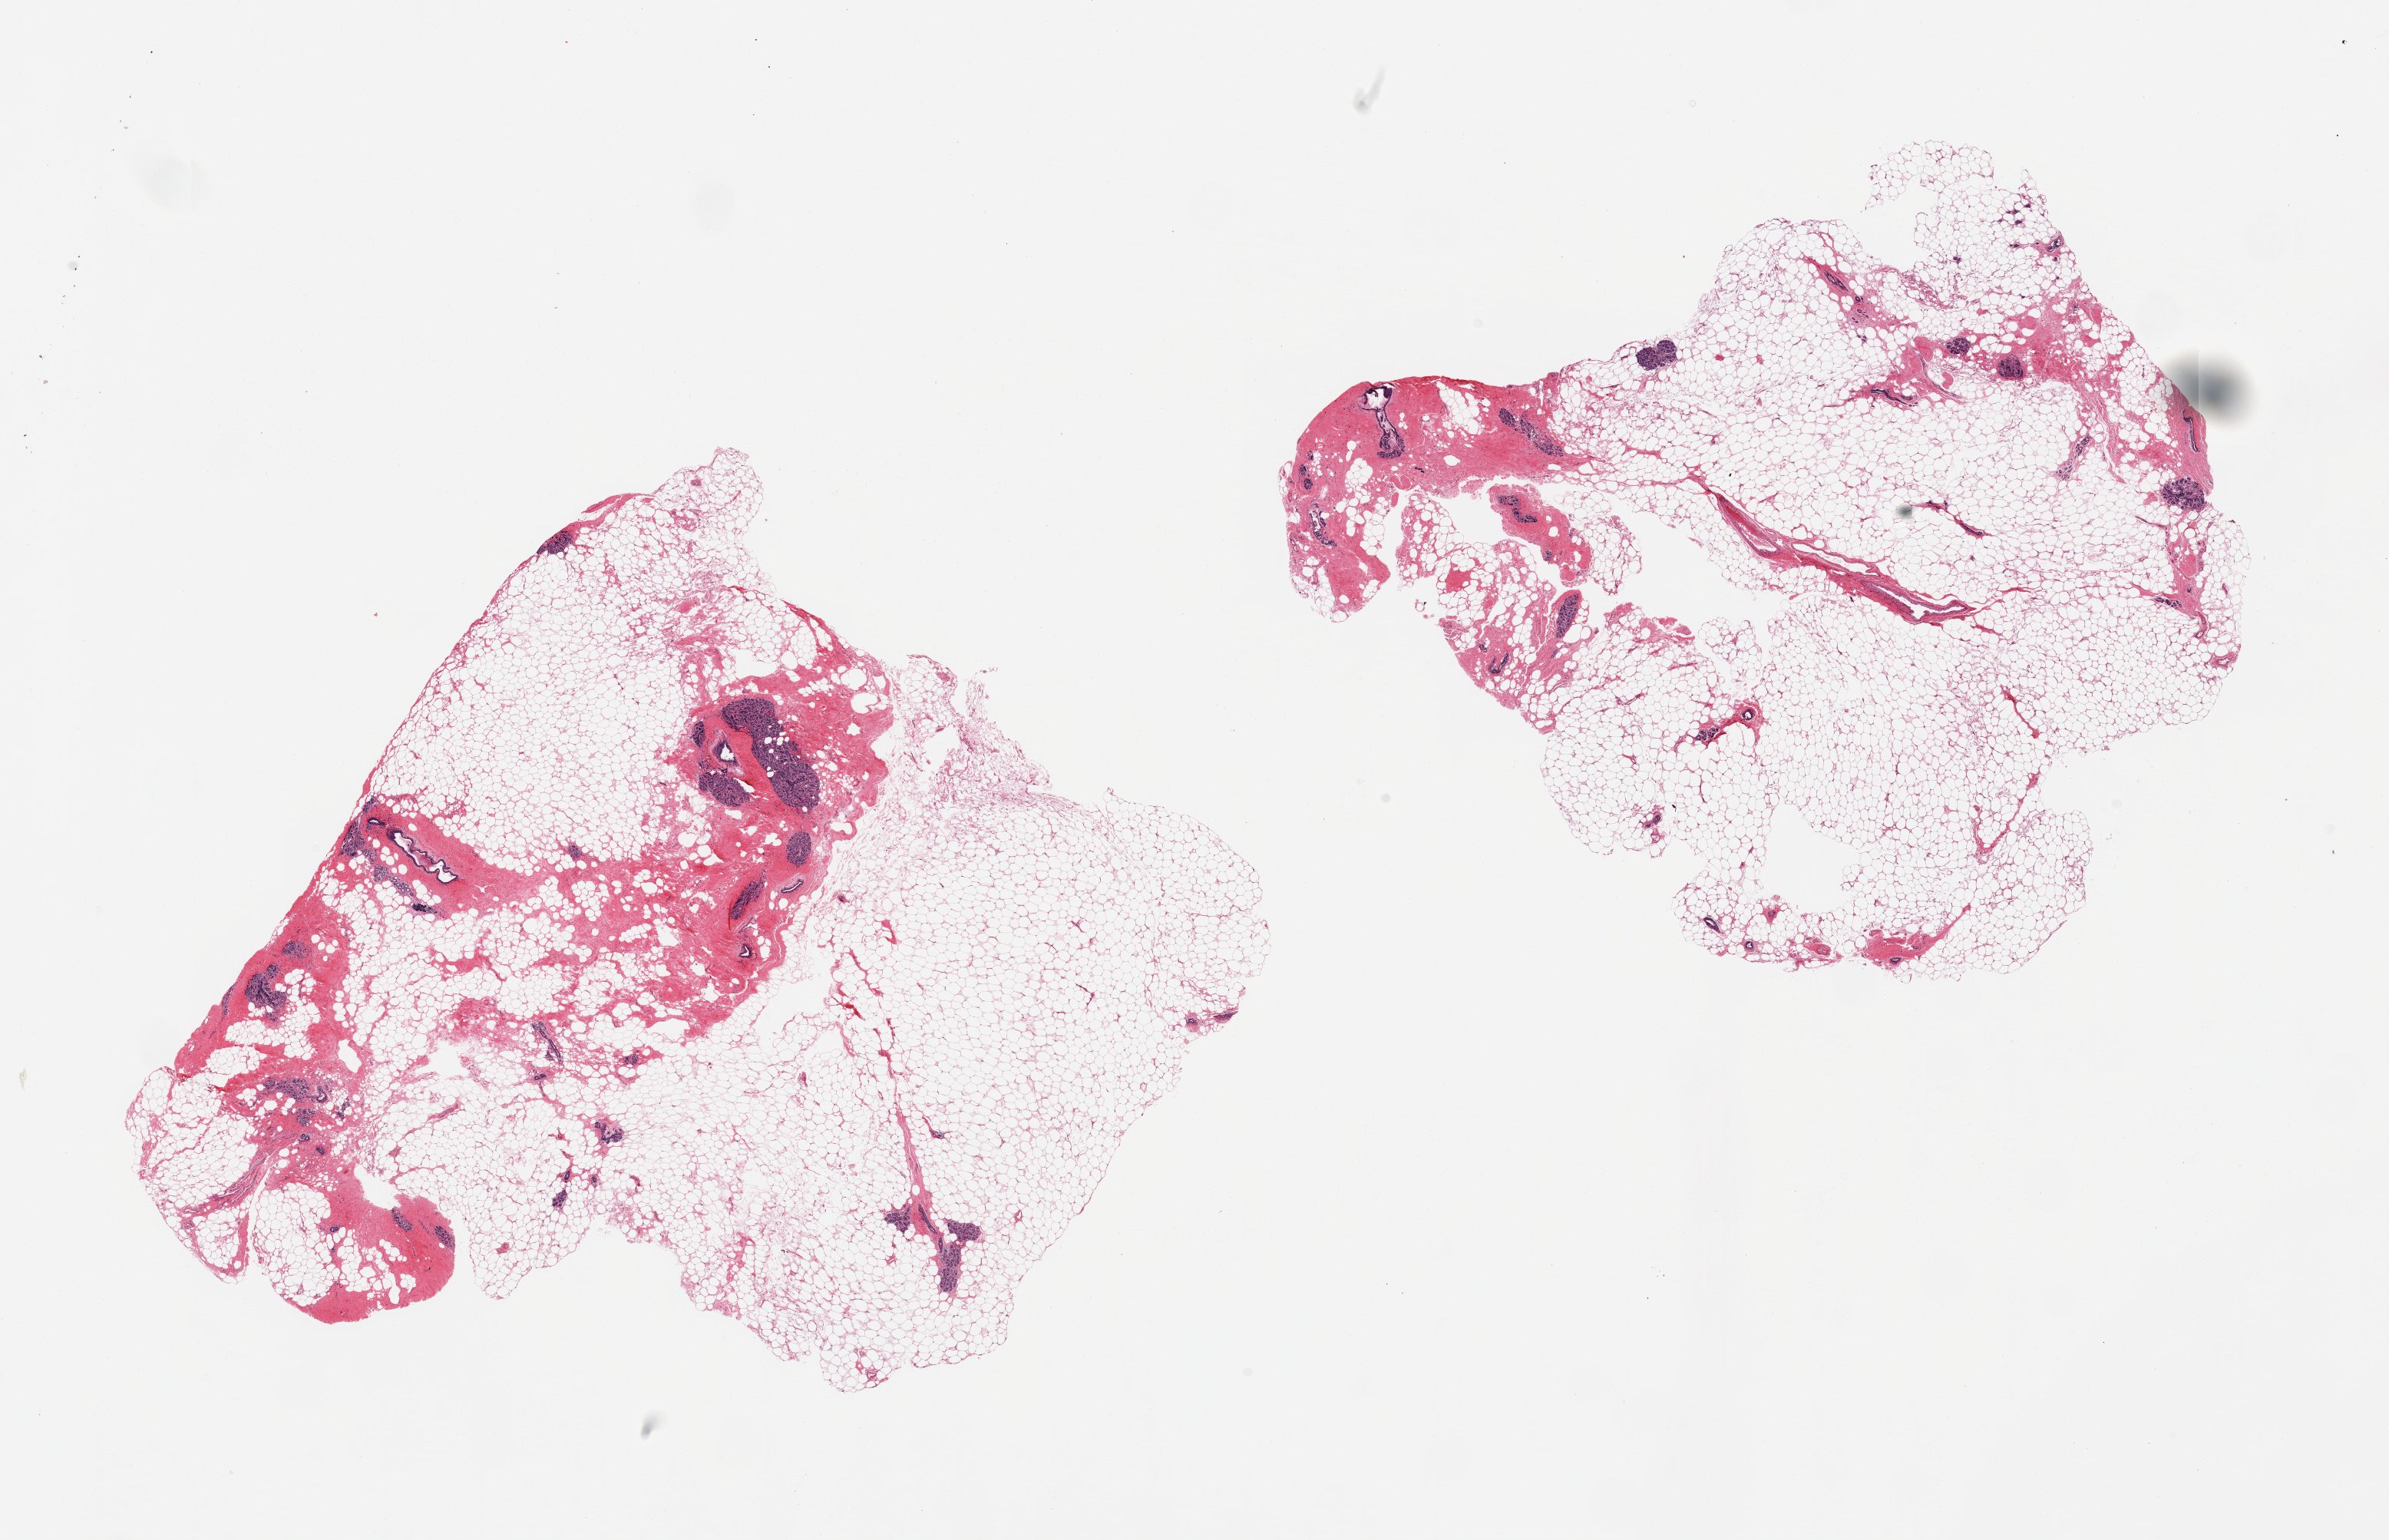
Hematoxylin and eosin (H&E) whole-slide image — shown as a low-resolution overview of the whole scanned area (about 24.6 x 15.9 mm, acquisition: 20x scan). PAXgene-fixed, paraffin-embedded tissue. Sampled site (target tissue): breast. Donor tissue sample. Donor sex: female.
Reviewer comment on this tissue sample: 2 pieces, well-defined TDLUs.